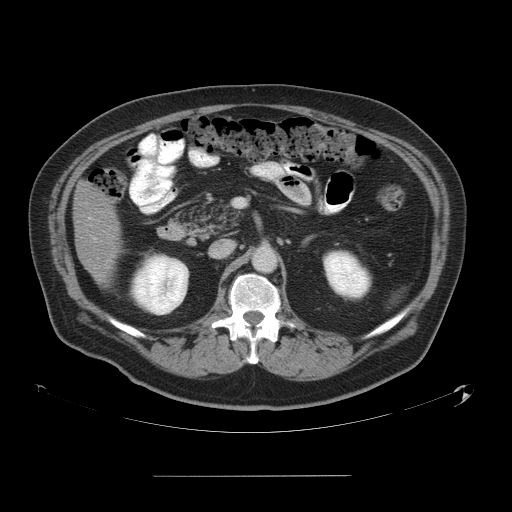
Contrast-enhanced abdominal CT, one axial slice; slice 24 of 58 in the series (ordered by position); 120 kVp; soft-tissue window (W 400 / L 40 HU); 5 mm slice thickness; 512 × 512 image matrix, field of view 480 × 480 mm. Male patient, age 63 years. Case-level facts recorded for this patient, not image findings: diagnosis: colorectal cancer liver metastases, imaged before liver resection; multiple liver metastases: no; largest metastasis: 4.2 cm.
Structures marked on this image (outlined manually by an expert reader):
- liver: box from (x=73, y=185) to (x=118, y=280) px
- planned liver remnant (the part of the liver to remain after resection): (x=73, y=184)–(x=118, y=281)
- portal vein (with intrahepatic branches): (x=89, y=217)–(x=91, y=220)